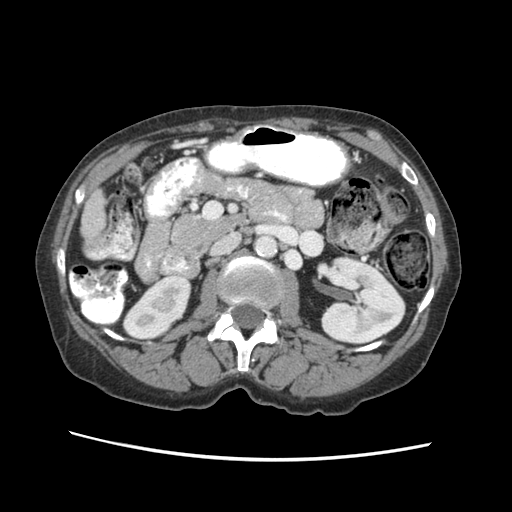
Contrast-enhanced abdominal CT (liver protocol), one axial slice; position 8 of 63 along the scan axis; soft-tissue window (W 400 / L 40 HU); 2.5 mm slice thickness; 512 × 512 image matrix. Case-level facts recorded for this patient, not image findings: diagnosis: hepatocellular carcinoma (patient treated with transarterial chemoembolisation; whether this scan precedes or follows treatment is not stated here); TNM stage (as recorded): Stage-I; Child-Pugh class: B; tumour differentiation: well differentiated; tumour nodularity: uninodular.
Outlined on this slice (semi-automatic segmentation, software-assisted and operator-edited):
- liver parenchyma outside the tumour (the mass and vessels are separate outlines, so this box may not span the whole liver): bounding box (x1, y1, x2, y2) in pixels: (80, 186, 108, 246)